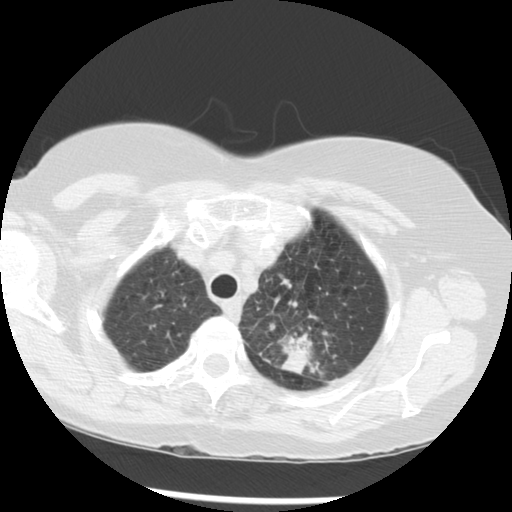
Low-dose screening chest CT, one axial slice; position 239 of 283 along the scan axis; lung window (W 1500 / L -600 HU); 2.5 mm slice thickness; 512 × 512 image matrix, field of view 330 × 330 mm.
Annotated regions visible in this slice (outlined manually by an expert reader):
- lesion 1 (tumor, upper lobe of left lung): bounding box [x1, y1, x2, y2] px = [282, 332, 314, 375]